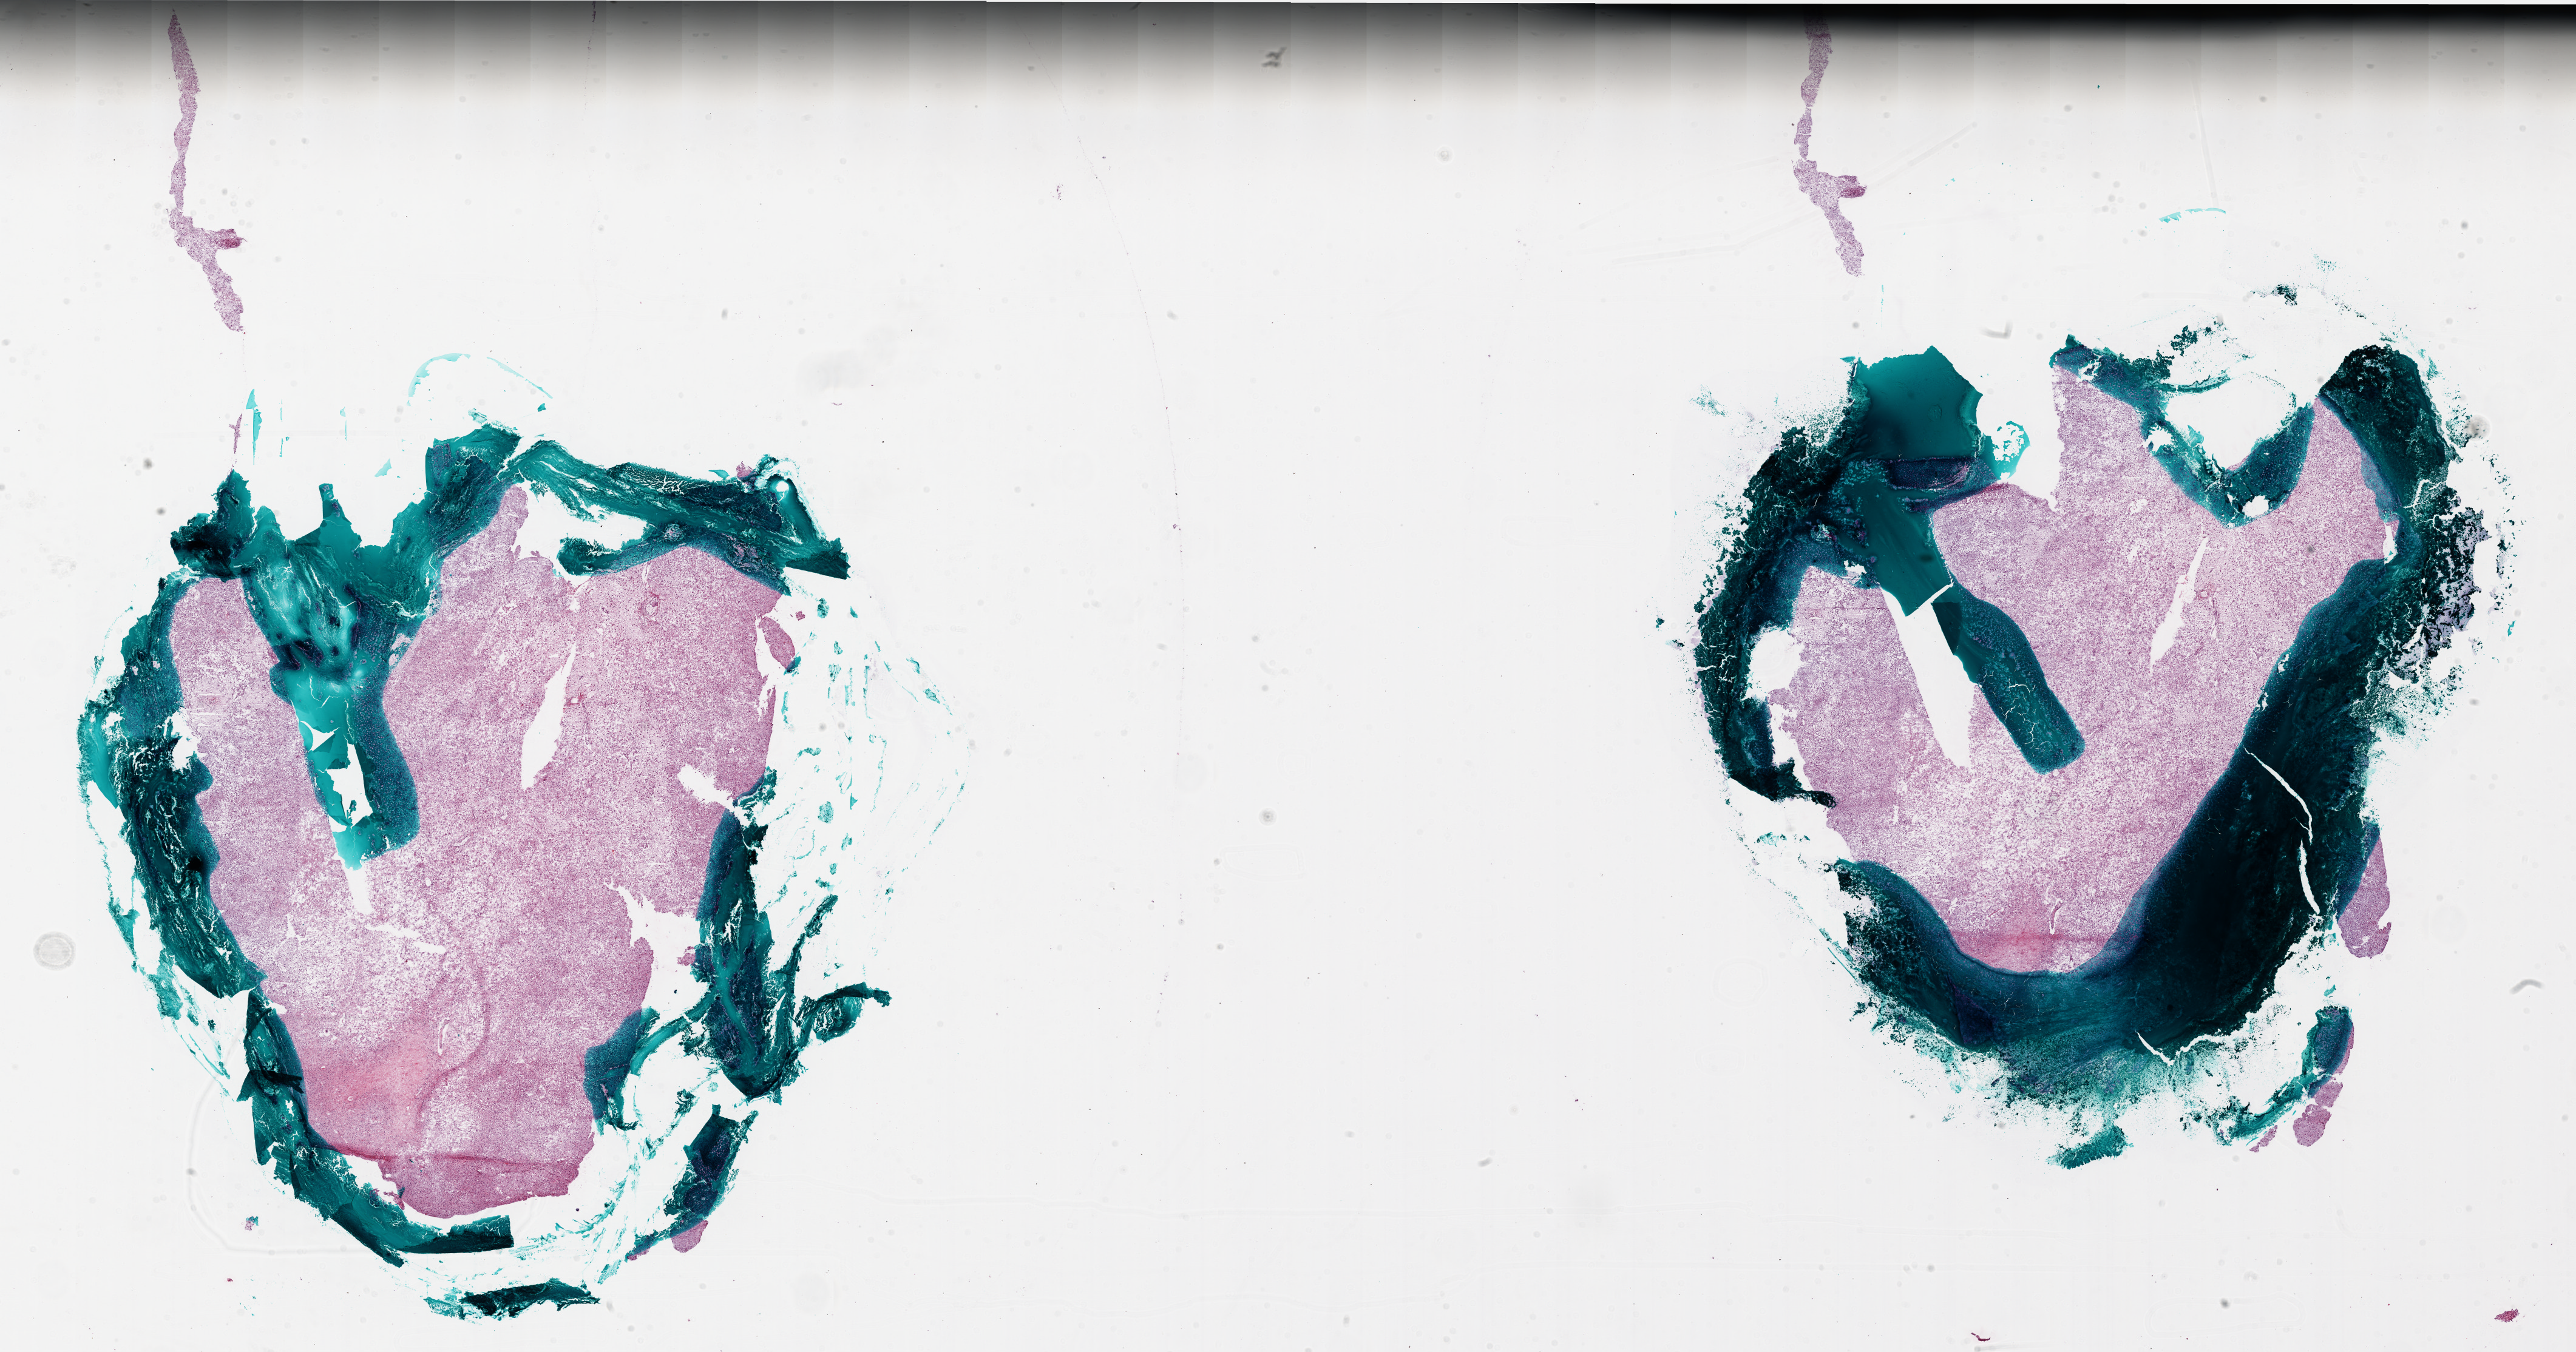
Whole-slide histology image, Hematoxylin and eosin (H&E) stained, shown as a low-resolution overview of the whole scanned area (about 34.0 x 17.8 mm); frozen section from the bottom of the tissue portion; sample: primary tumour, brain. Male, age 52 years at initial diagnosis. Pathologist review of this section (percent, as recorded): tumour cells 90%, tumour nuclei 100%.
Histologic diagnosis: Glioblastoma.